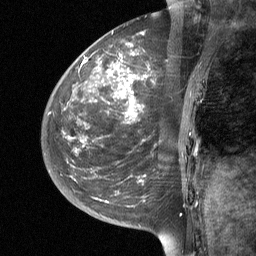
Breast MRI (dynamic contrast-enhanced), one sagittal slice; slice 15 of 64 in the series (ordered by position); dynamic contrast-enhanced study with each time point stored as its own series, time point 2 of 3 at this slice position (early post-contrast, ordered by acquisition time); 1.5 T; TE 4.8 ms, TR 27 ms; 2 mm slice thickness; 256 × 256 image matrix. Female patient, age 42 years. From the clinical record (not read from this slice): setting: breast cancer imaged before/during neoadjuvant chemotherapy; receptor status: triple-negative.
Structures marked on this image (semi-automatically segmented with operator editing):
- analysis volume of interest (the breast-tissue region the enhancement analysis was run in; not a lesion): box from (x=43, y=29) to (x=203, y=190) px
- tumour enhancement mask (voxels above the 90 % enhancement threshold inside the analysis volume of interest): (x=82, y=32)–(x=146, y=140)